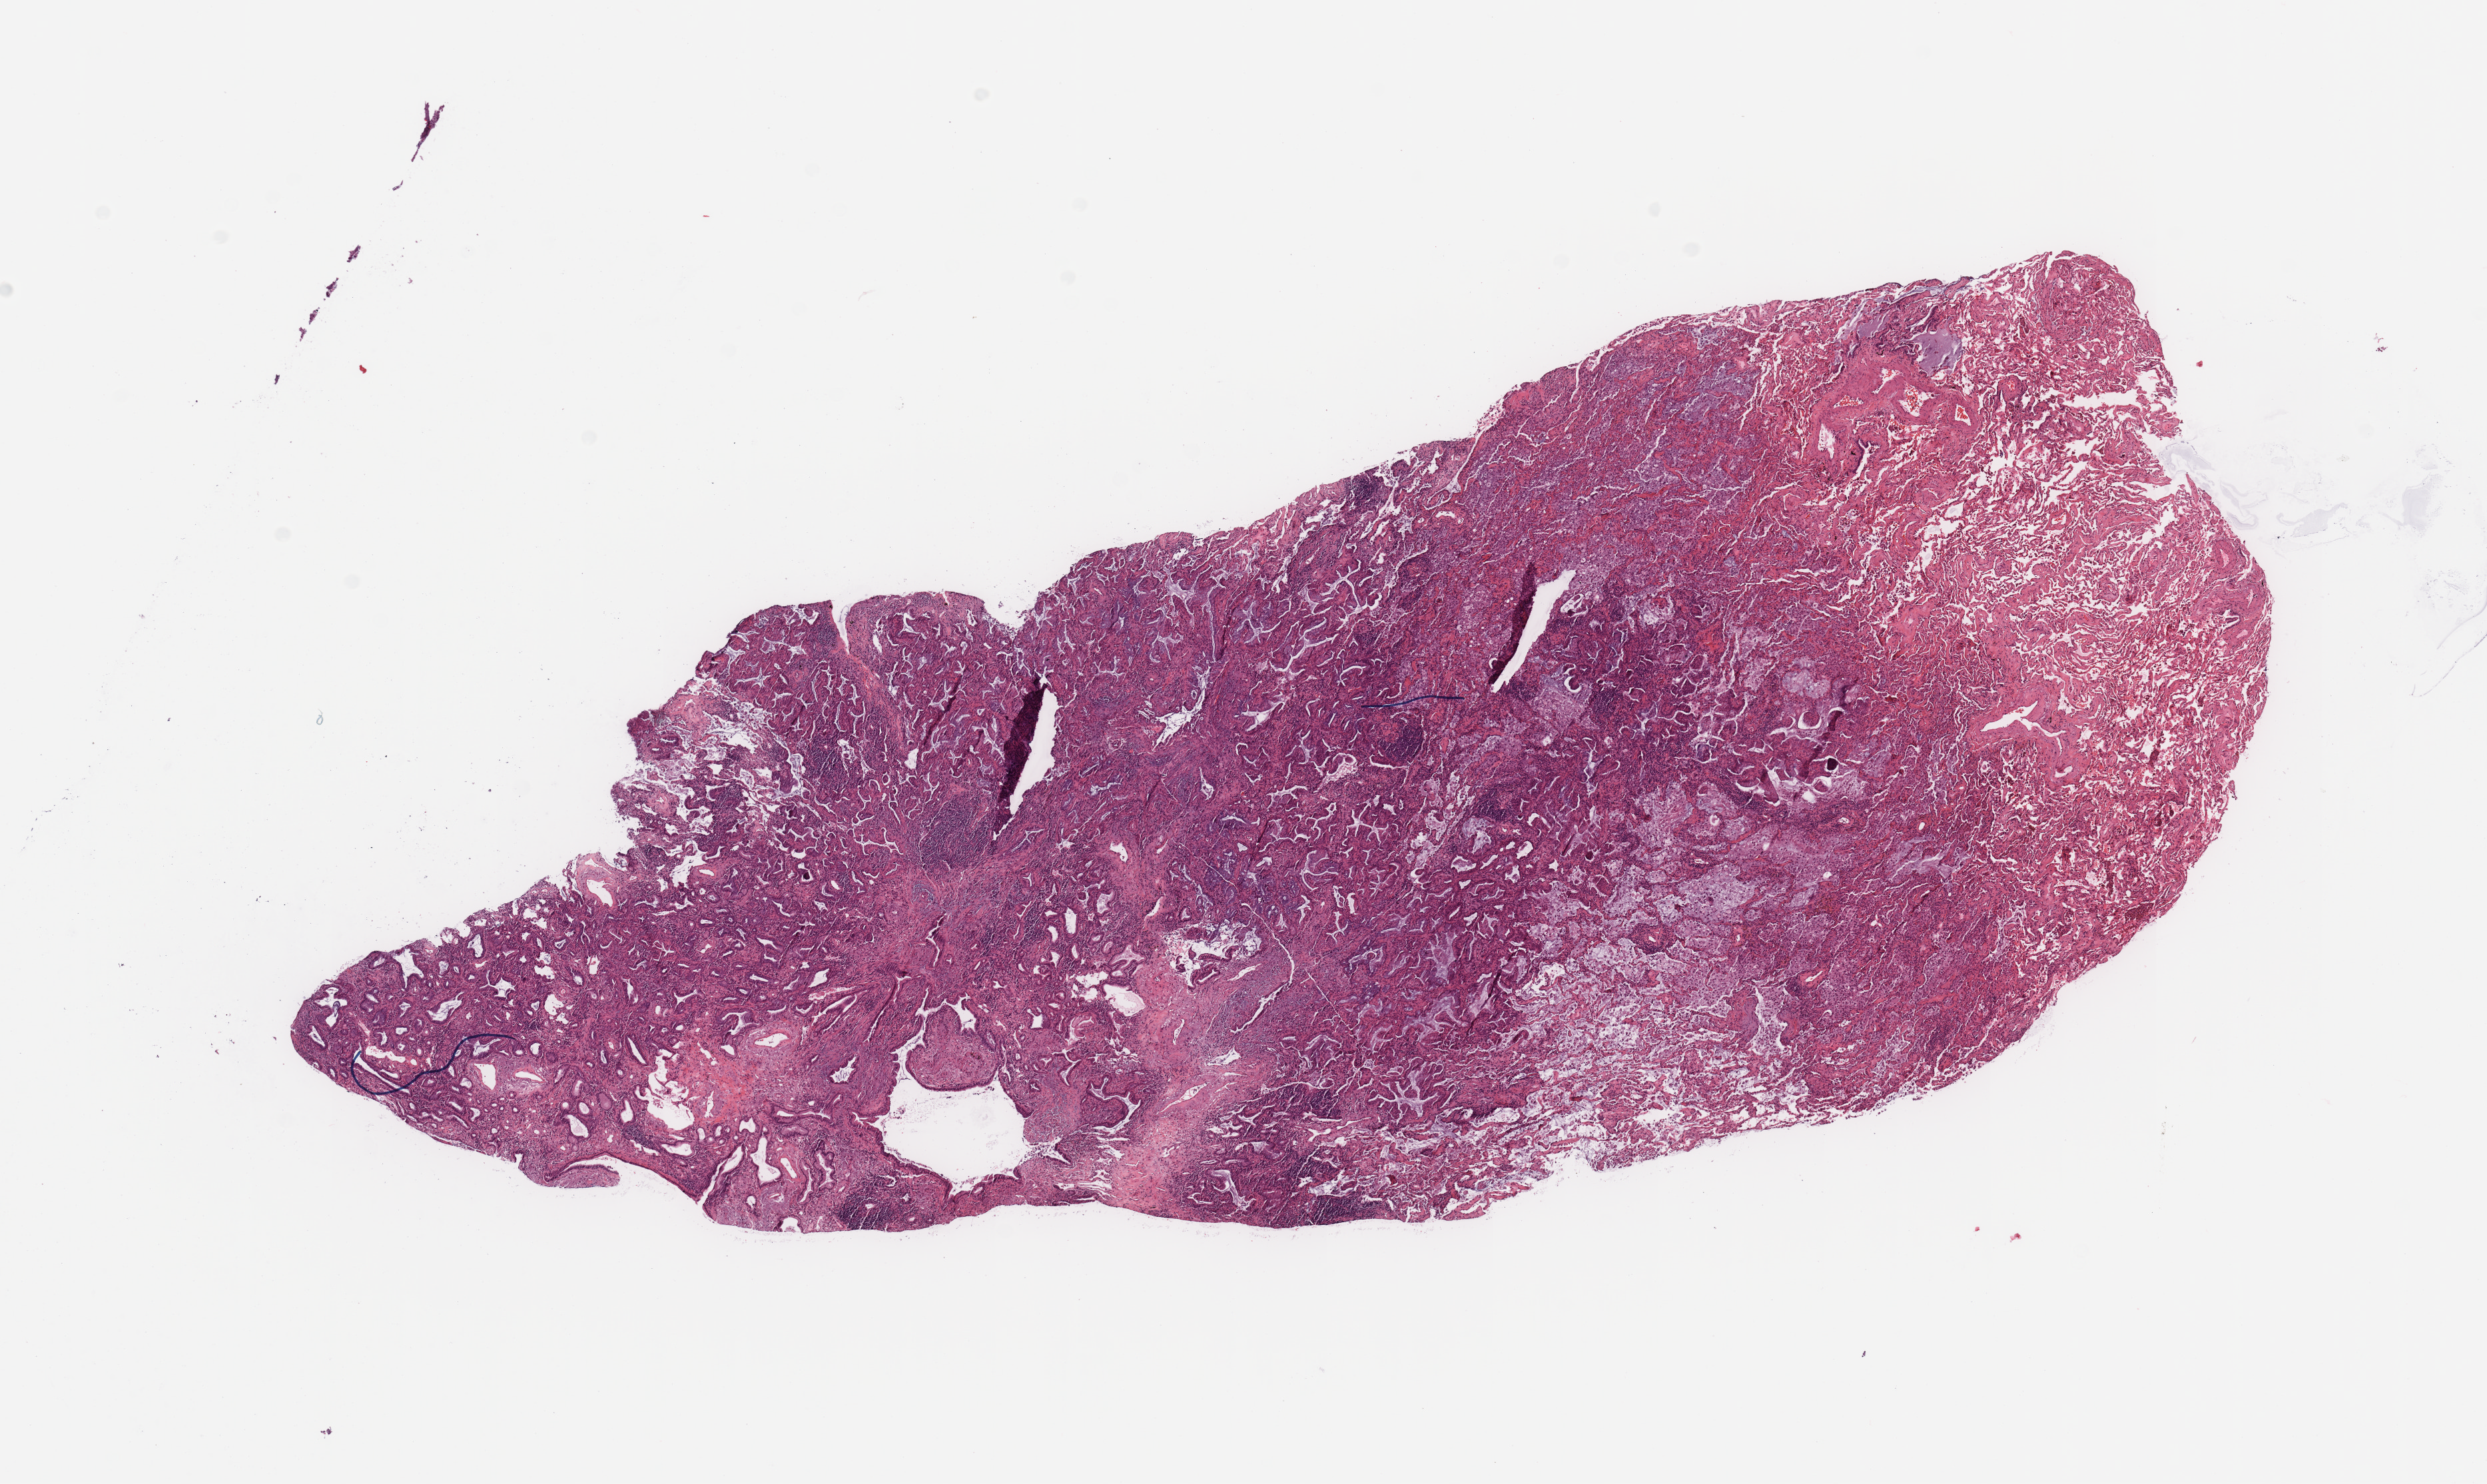
H&E whole-slide image, whole scanned area (about 14.8 x 8.8 mm) shown as a low-resolution overview. Tumour tissue sample, lung. Female, 78 y/o. Histologic grade: G1 (well differentiated).
Histologic diagnosis: Adenocarcinoma, NOS. AJCC pathologic stage: IA.